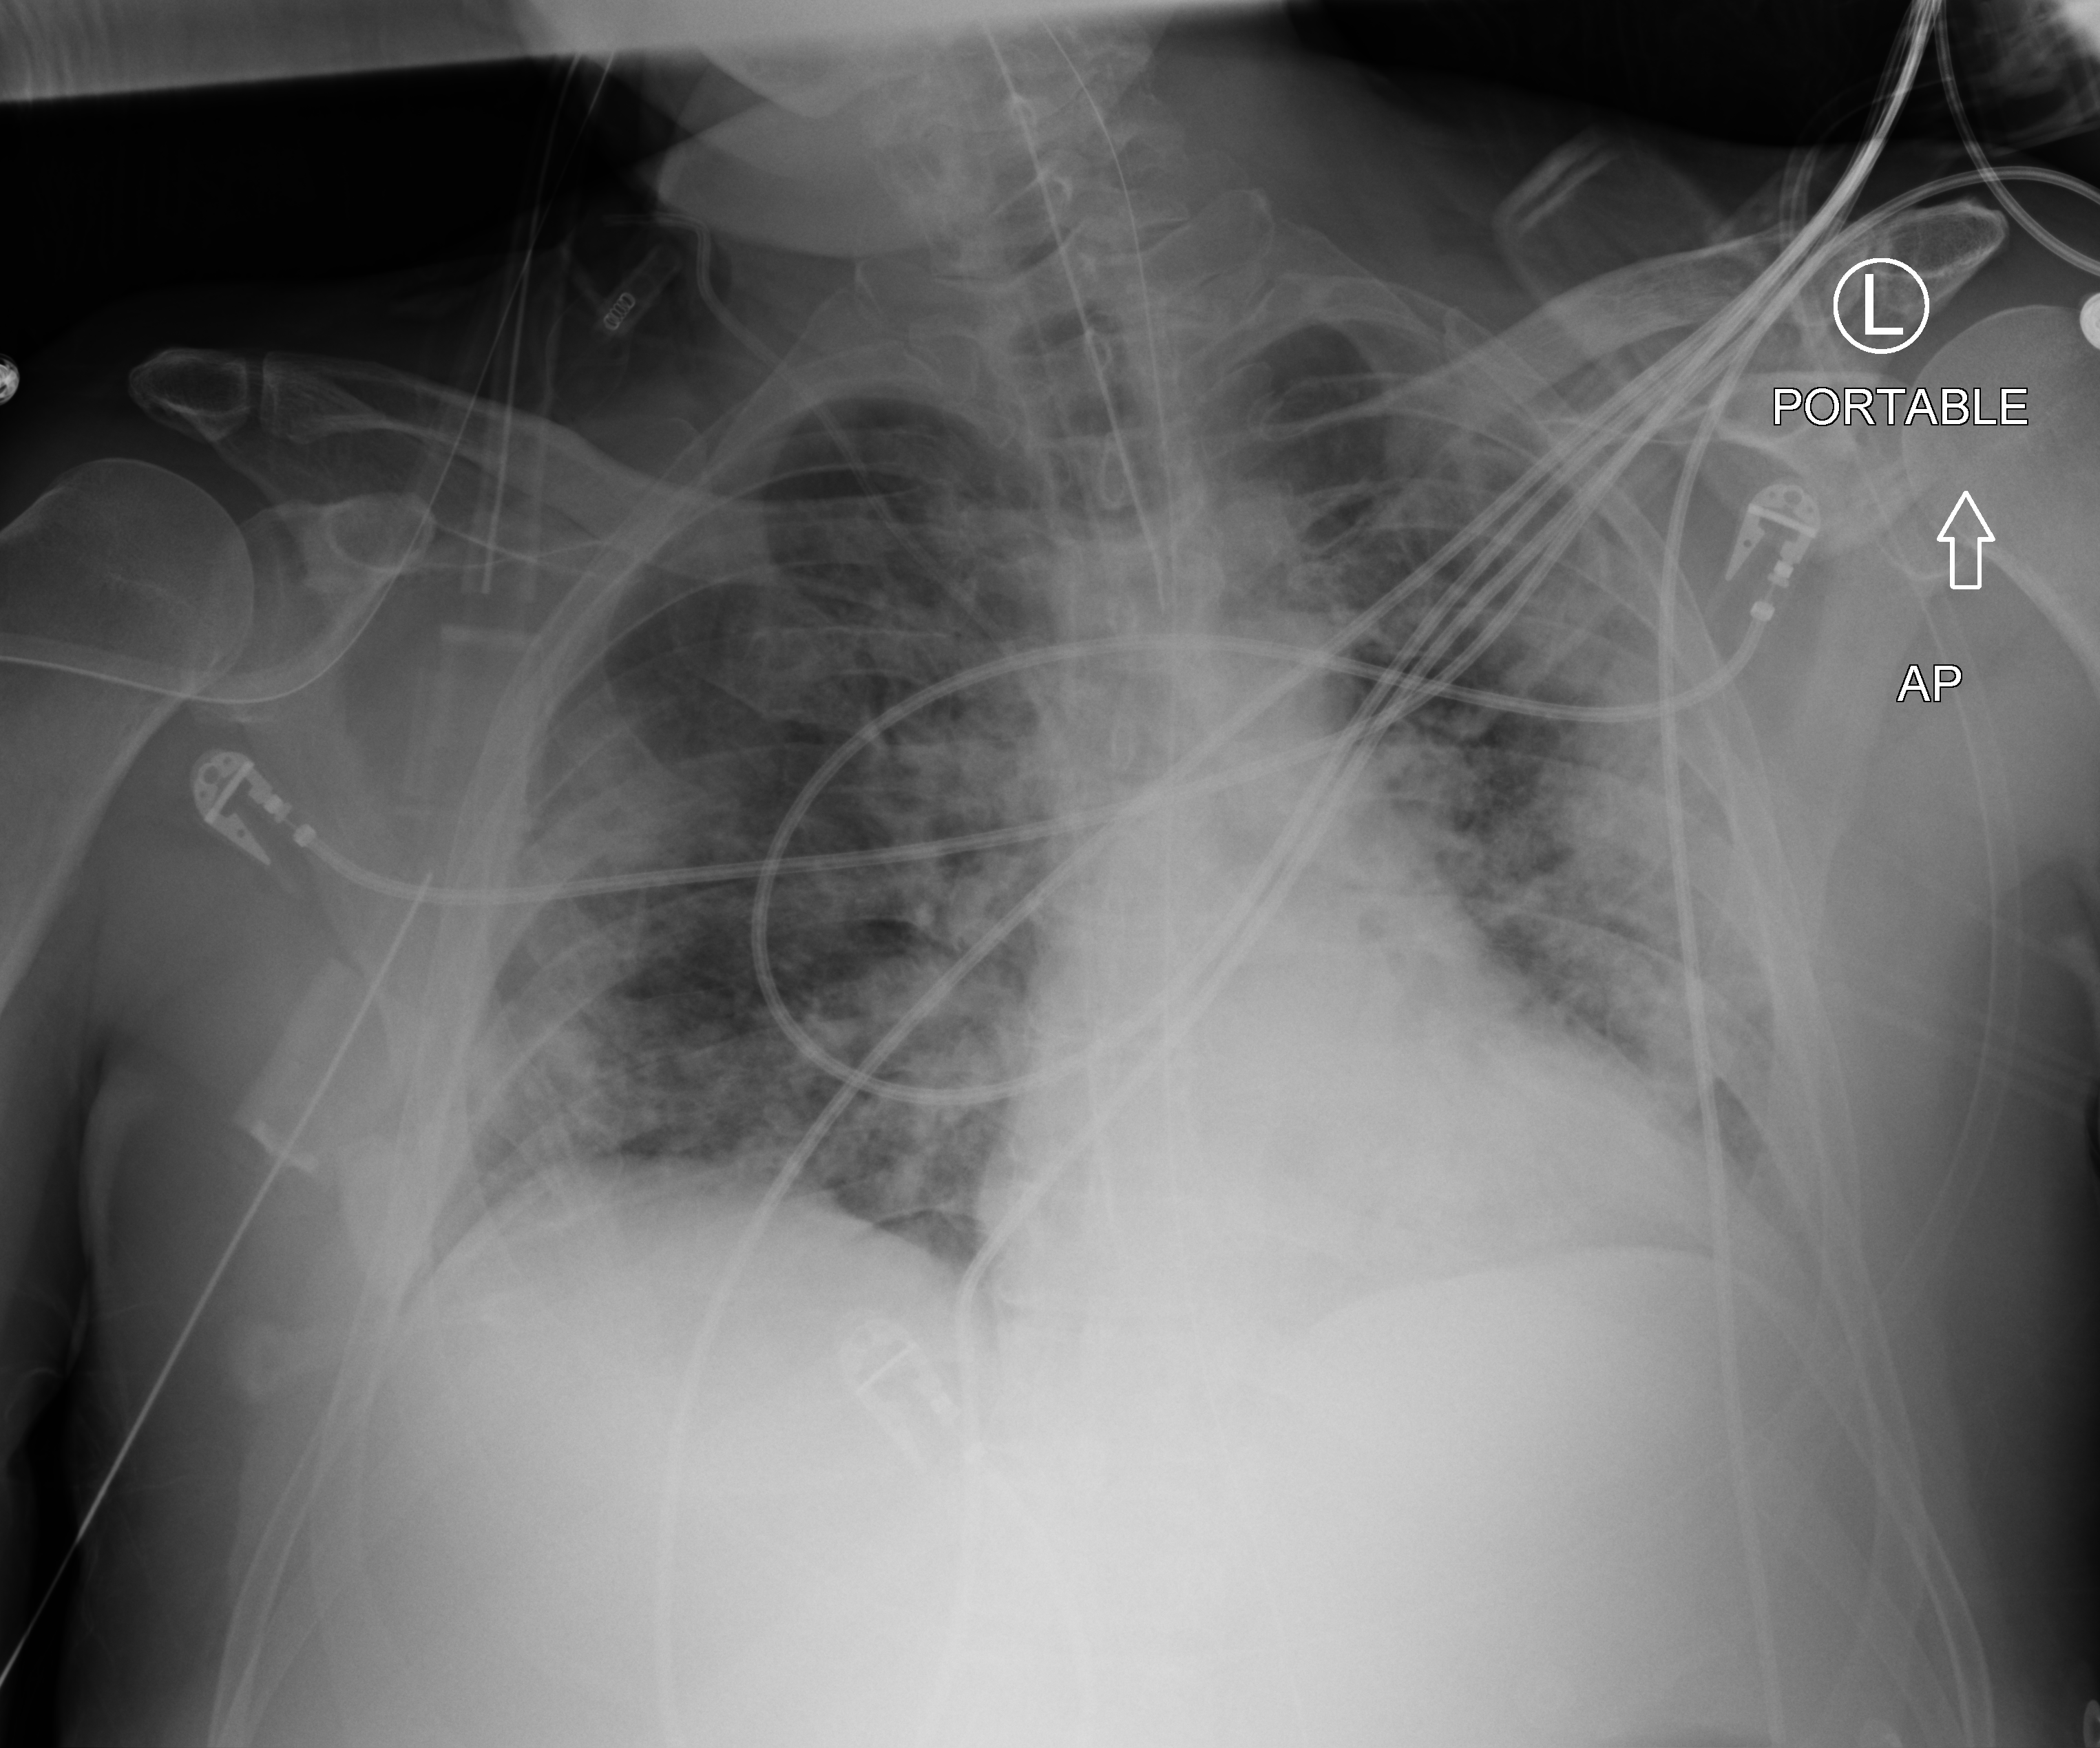
Bedside chest radiograph (computed radiography). Patient hospitalised with COVID-19; male, aged 18–59 years.
Hospital-stay facts (about this admission, not read from this image; timing relative to this image not recorded): admitted to intensive care during this hospital stay: yes; mechanically ventilated during this hospital stay: yes.